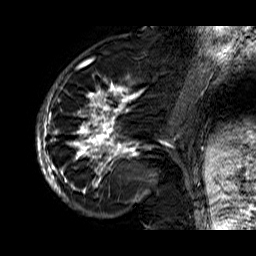
Breast MRI (dynamic contrast-enhanced), one sagittal slice; position 20 of 60 along the scan axis; dynamic contrast-enhanced series, time point 2 of 6 at this slice position (early post-contrast); 1.5 T; TE 6.3 ms, TR 32.9 ms; 256 × 256 image matrix. Female patient. Case-level facts recorded for this patient, not image findings: setting: breast cancer imaged before/during neoadjuvant chemotherapy; receptor status: HR-positive, HER2-negative.
Annotated regions visible in this slice (semi-automatic segmentation, software-assisted and operator-edited):
- analysis volume of interest (the breast-tissue region the enhancement analysis was run in; not a lesion): bounding box [x1, y1, x2, y2] px = [36, 74, 176, 210]
- tumour enhancement mask (voxels above the 100 % enhancement threshold inside the analysis volume of interest): [37, 74, 176, 205]